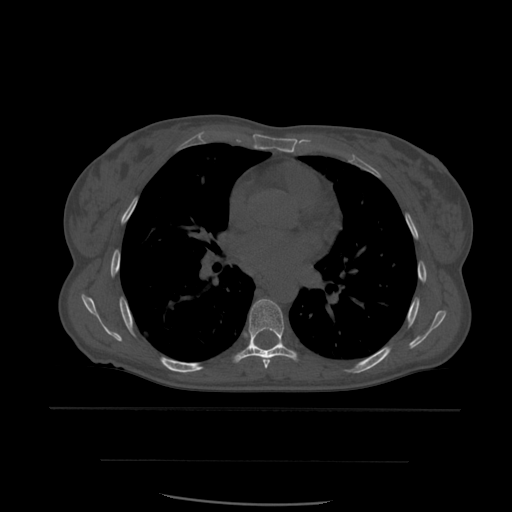
CT including the spine, one axial slice; slice 377 of 574 in the series (ordered by position); bone window (W 1800 / L 400 HU); 1.25 mm slice thickness; 512 × 512 image matrix, field of view 392 × 392 mm. Patient age 48 years. From the clinical record (not read from this slice): primary cancer: lung; vertebrae with lytic lesions (as recorded): T11.
Annotated regions visible in this slice (semi-automatically segmented with operator editing):
- T6 vertebra: bounding box <262,358,271,369> (left, top, right, bottom; pixels)
- T7 vertebra: <233,299,298,363>